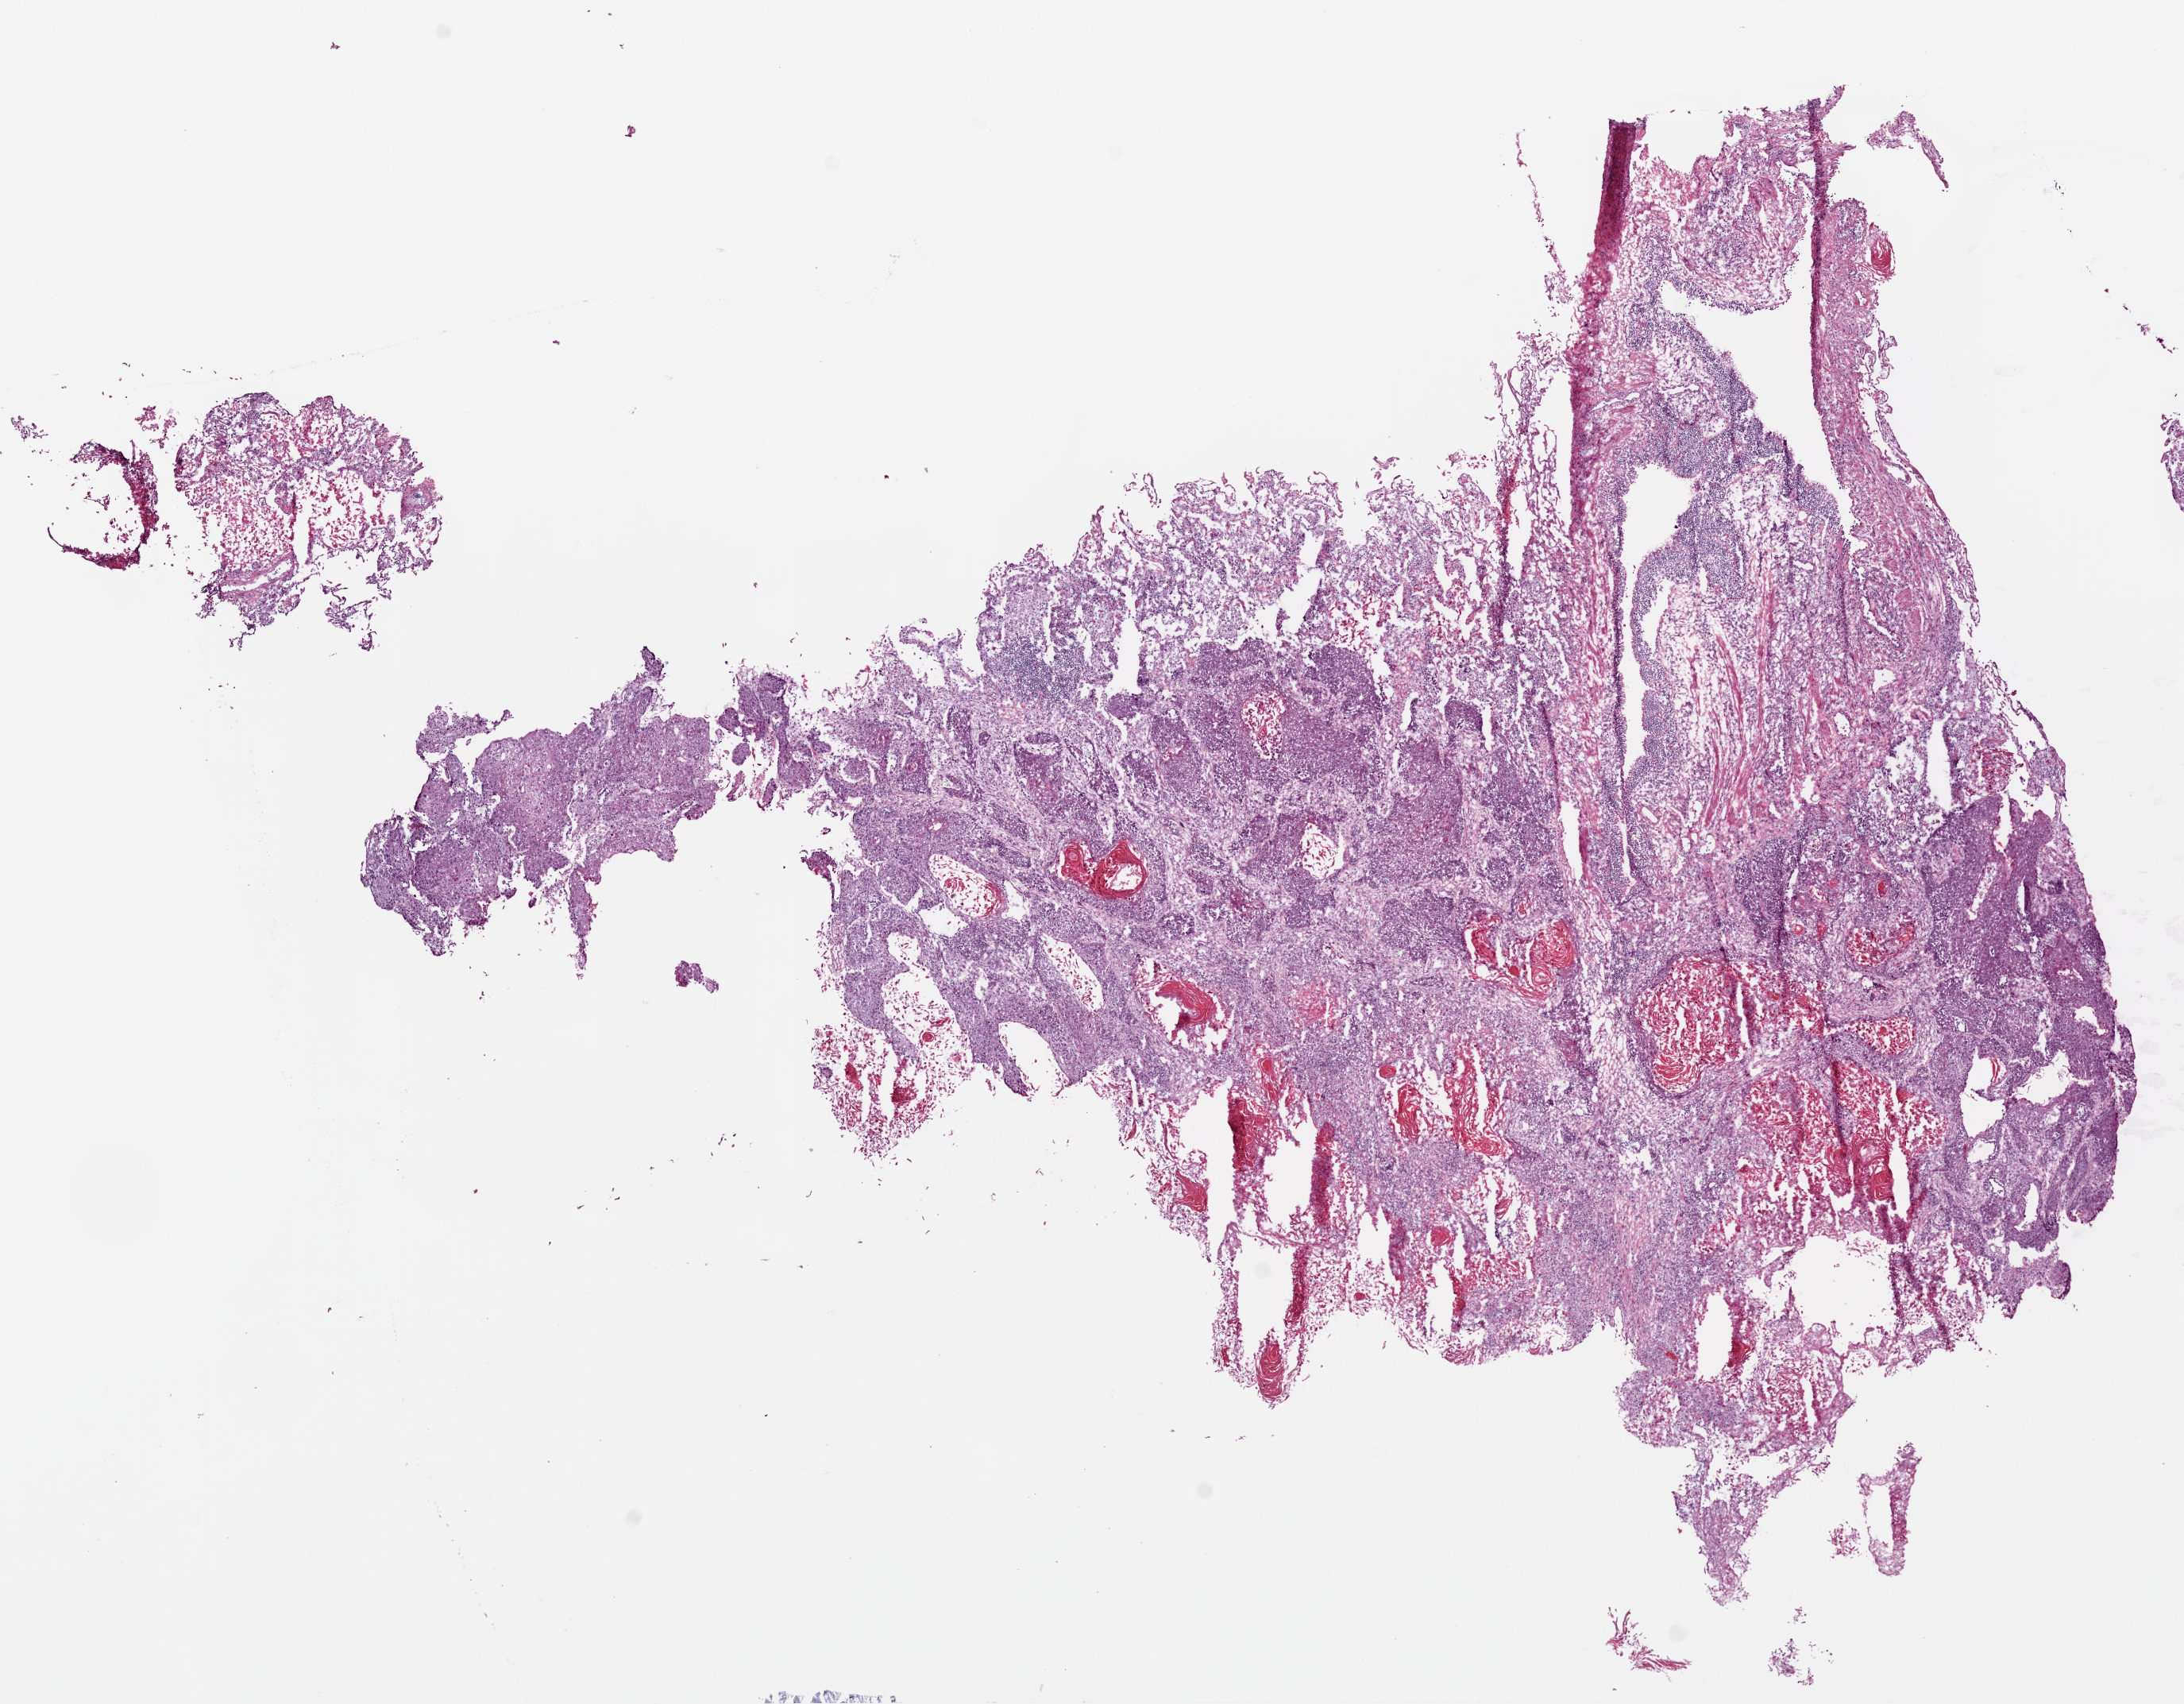
Whole-slide histology image, H&E-stained, low-resolution overview of the scanned area, about 11.0 x 8.6 mm (acquisition: 20x scan), frozen section from the bottom of the tissue portion, sample: primary tumour, lung. Female, age 78 years at initial diagnosis. Pathologist review of this section (percent, as recorded): tumour cells 45%, tumour nuclei 70%, normal cells 15%, stromal cells 20%, necrosis 20%.
Laterality: right. TNM: T2 N0 M0. AJCC pathologic stage: IB (6th edition). Histologic diagnosis: Squamous cell carcinoma, large cell, nonkeratinizing, NOS (upper lobe, lung).